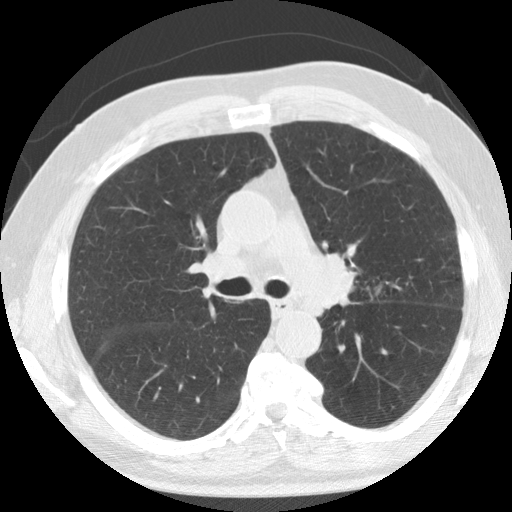
Low-dose screening chest CT, one axial slice. Position 84 of 133 along the scan axis. Reconstruction kernel STANDARD. 120 kVp. Lung window (W 1500 / L -600 HU). 2.5 mm slice thickness. 512 × 512 image matrix.
Structures marked on this image (expert manual segmentation):
- lesion 1 (tumor, upper lobe of left lung): bounding box [x1, y1, x2, y2] px = [320, 253, 354, 307]